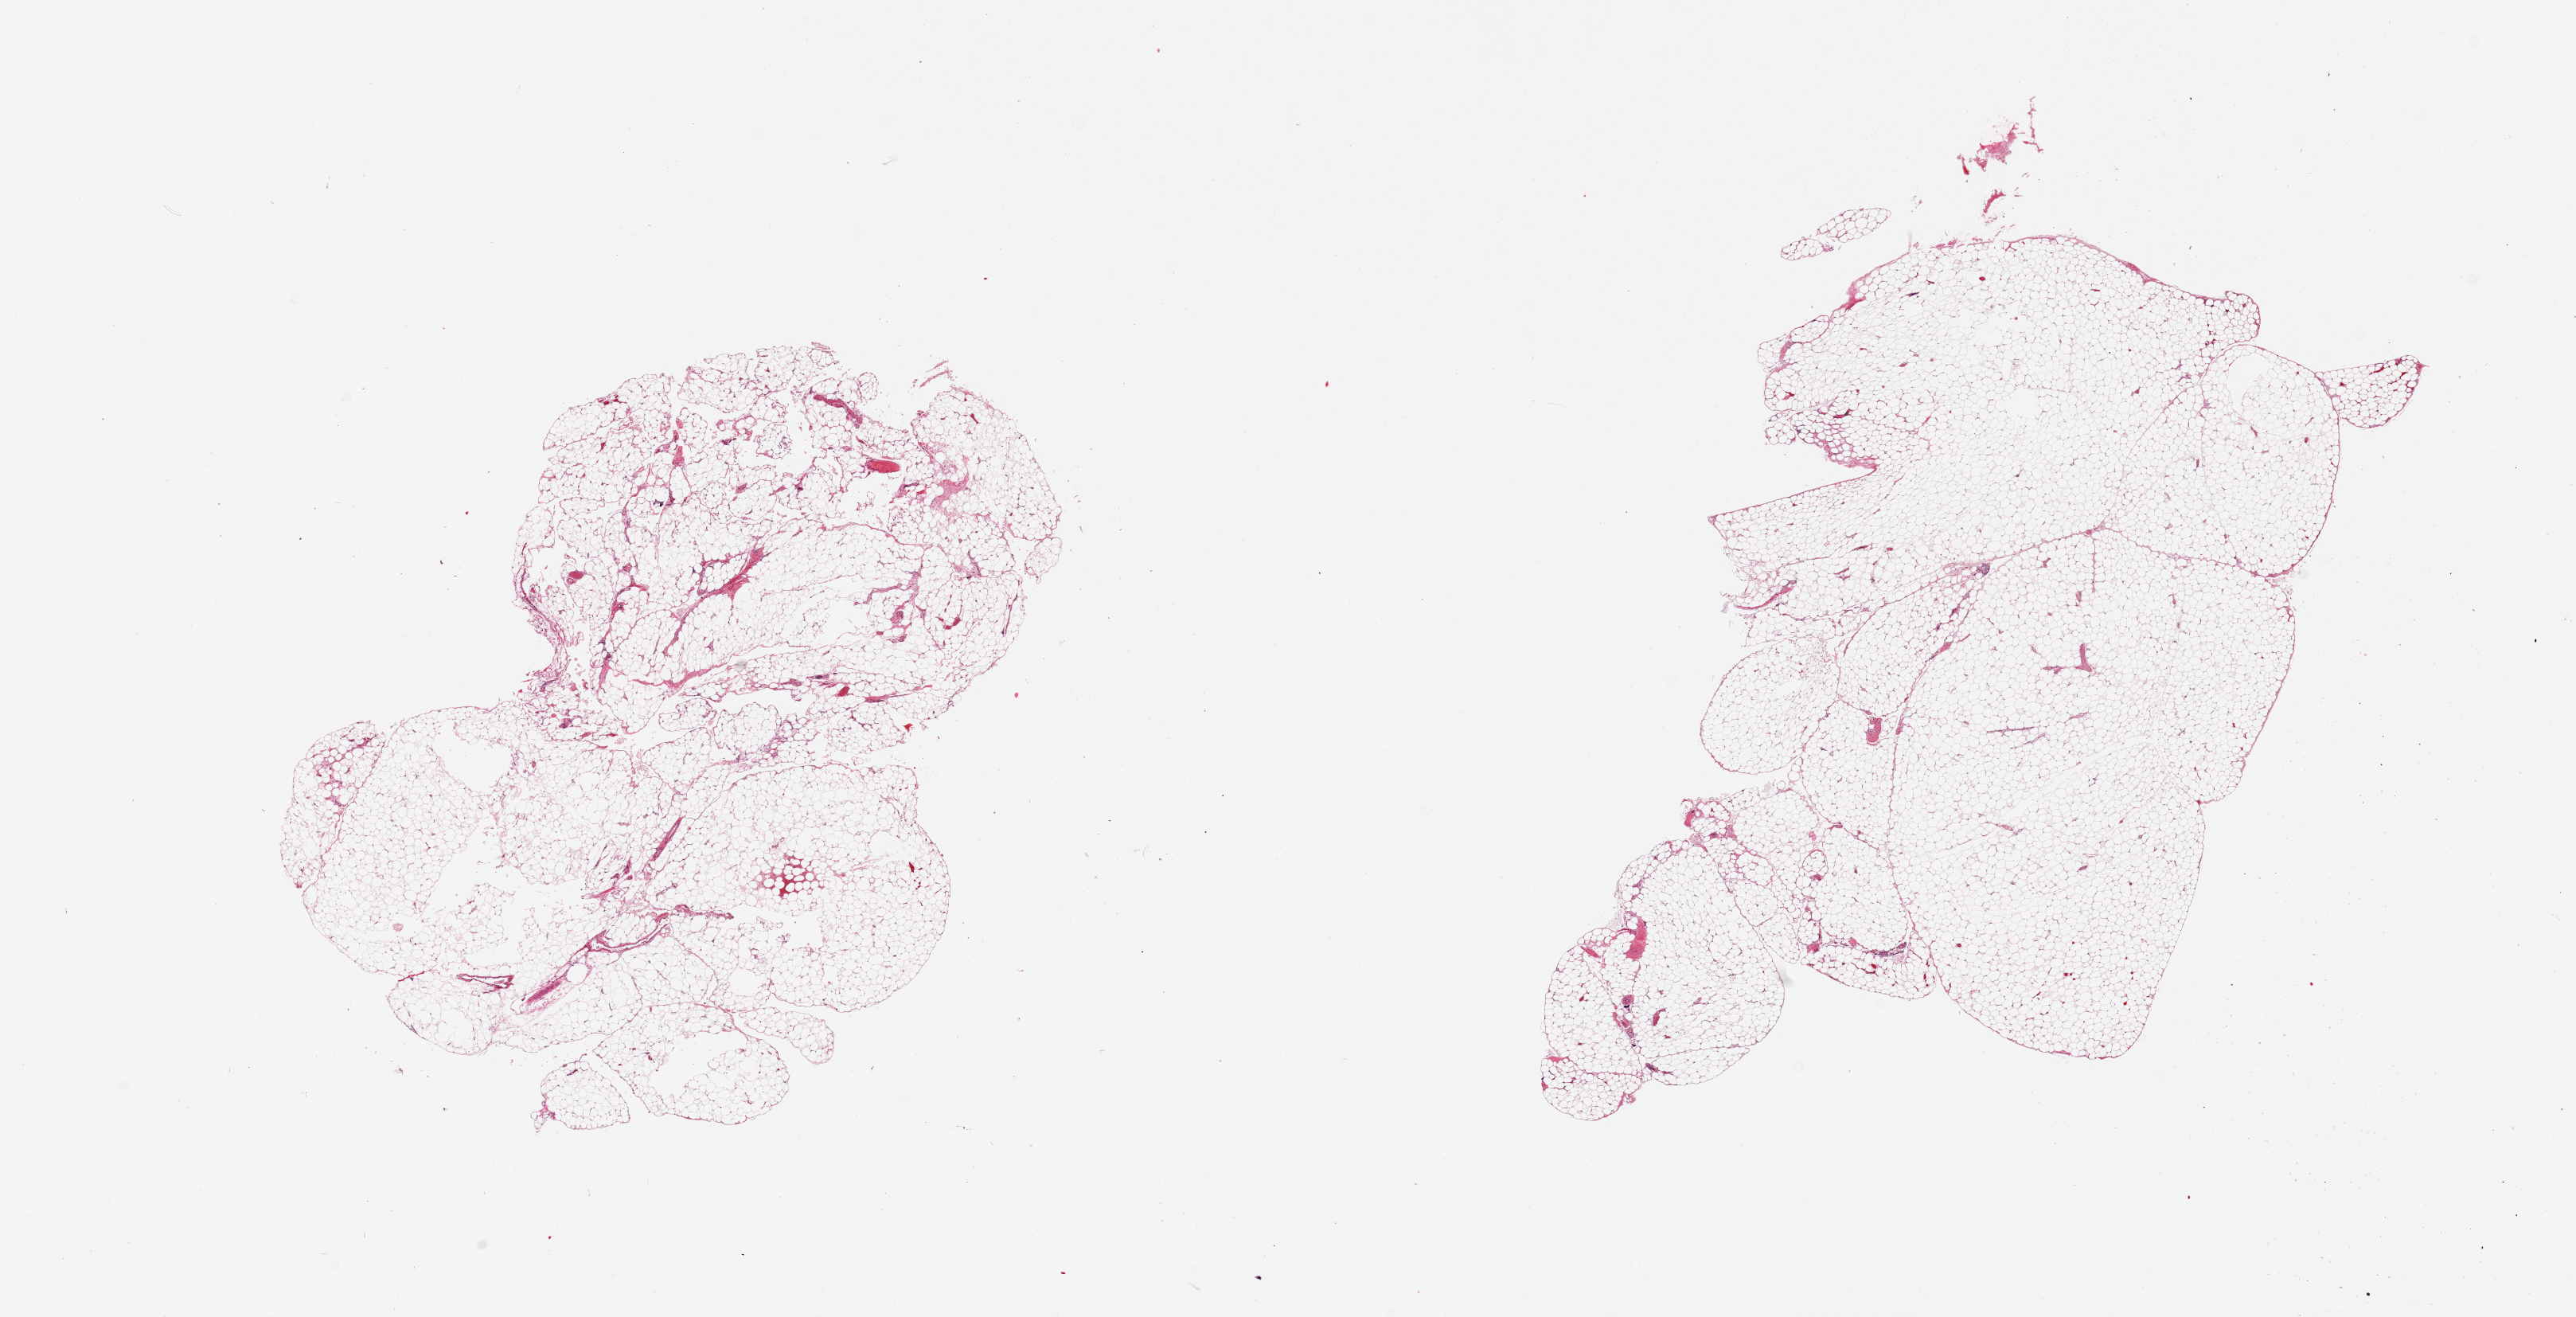
Whole-slide image, H&E stain, a low-resolution overview of the entire scanned area, about 25.6 x 13.1 mm. PAXgene-fixed, paraffin-embedded tissue. Target tissue: omentum. Tissue donor sample.
Review note (as recorded): 2 pieces, minimal fascia.